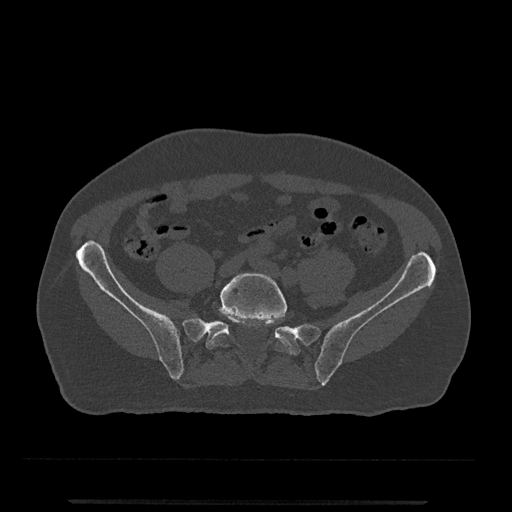
CT including the spine, one axial slice. Position 46 of 797 along the scan axis. 120 kVp. Bone window (W 1800 / L 400 HU). 0.5 mm slice thickness. 512 × 512 image matrix, field of view 419 × 419 mm. Patient: male, 63 years. Case-level facts recorded for this patient, not image findings: primary cancer: prostate.
Annotated regions visible in this slice (semi-automatically segmented with operator editing):
- L5 vertebra: box from (x=209, y=273) to (x=291, y=354) px